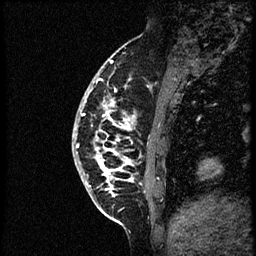
Breast MRI (dynamic contrast-enhanced), one sagittal slice; slice 16 of 56 in the series (ordered by position); dynamic contrast-enhanced study with each time point stored as its own series, time point 2 of 3 at this slice position (early post-contrast, ordered by acquisition time); 1.5 T; TE 4.2 ms, TR 21.3 ms; 2 mm slice thickness; 256 × 256 image matrix, field of view 200 × 200 mm. Female patient, age 41 years. From the clinical record (not read from this slice): setting: breast cancer imaged before/during neoadjuvant chemotherapy; receptor status: HER2-positive.
Structures marked on this image (semi-automatic segmentation, software-assisted and operator-edited):
- analysis volume of interest (the breast-tissue region the enhancement analysis was run in; not a lesion): bounding box <72,73,177,205> (left, top, right, bottom; pixels)
- tumour enhancement mask (voxels above the 100 % enhancement threshold inside the analysis volume of interest): <76,97,136,190>